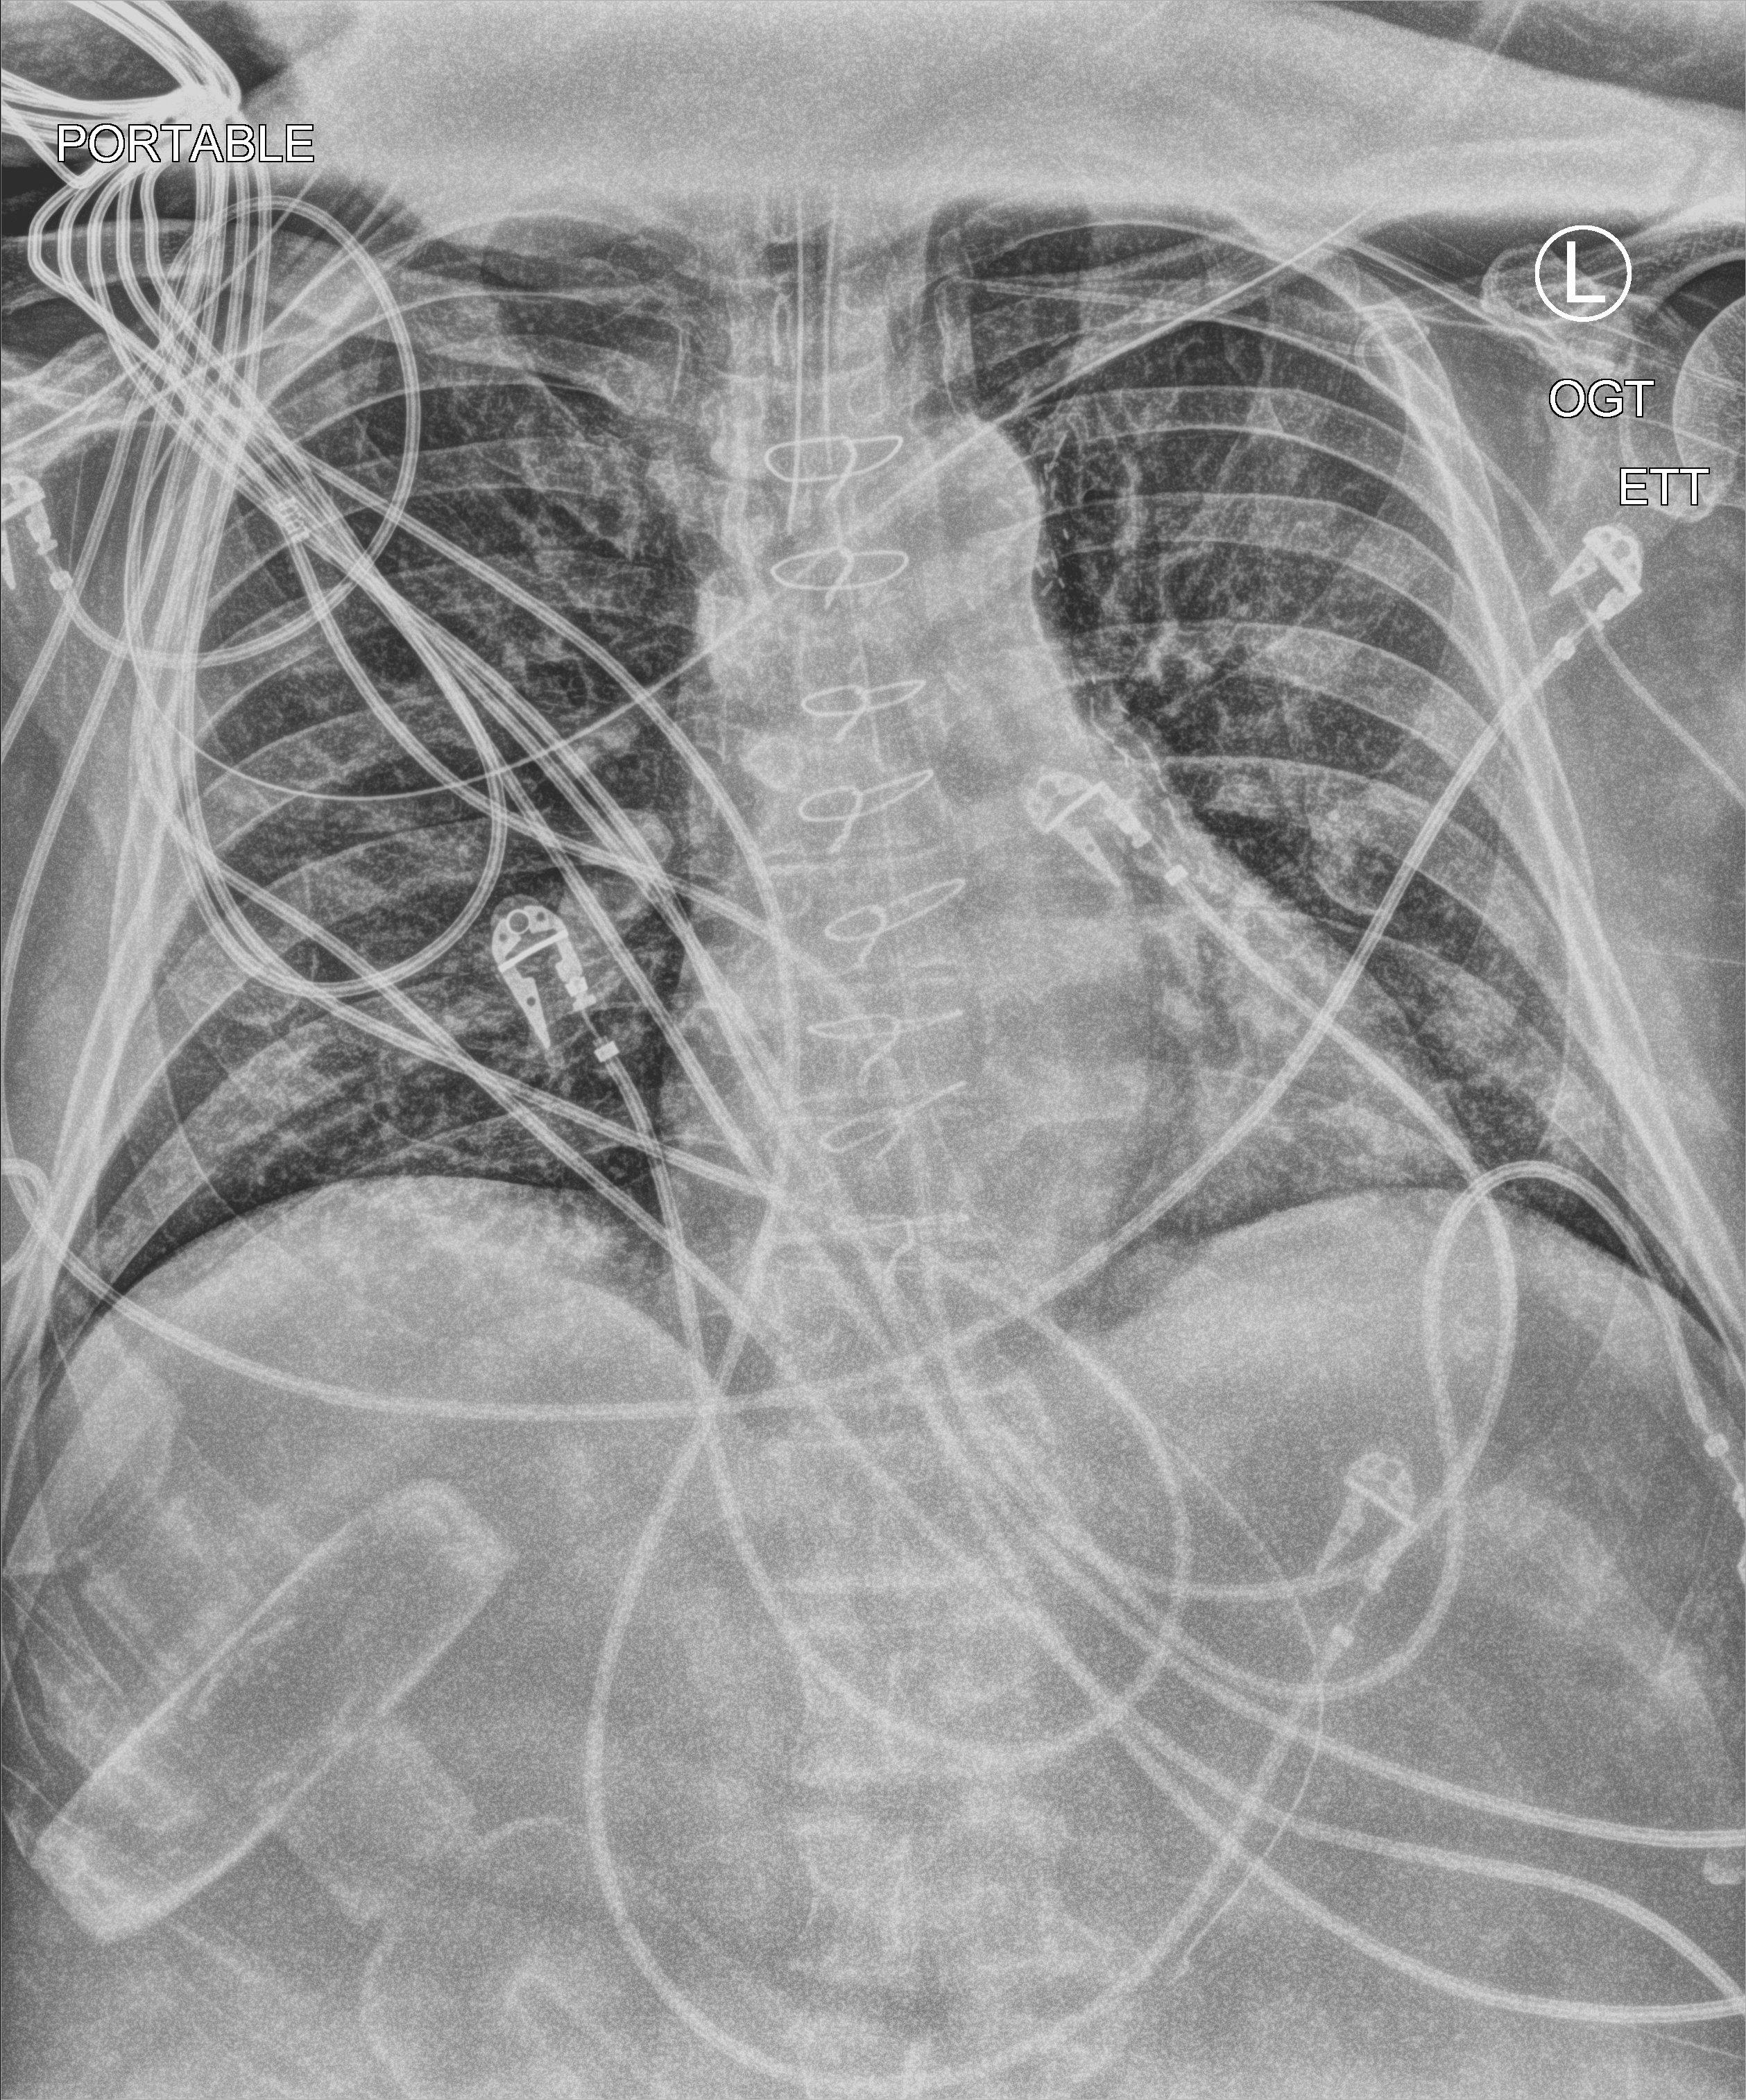
Bedside chest radiograph (computed radiography); anteroposterior (AP) projection. Patient hospitalised with COVID-19; male, aged 60–74 years.
Hospital-stay facts (about this admission, not read from this image; timing relative to this image not recorded):
- admitted to intensive care during this hospital stay: yes
- other chronic lung disease (admission record): no